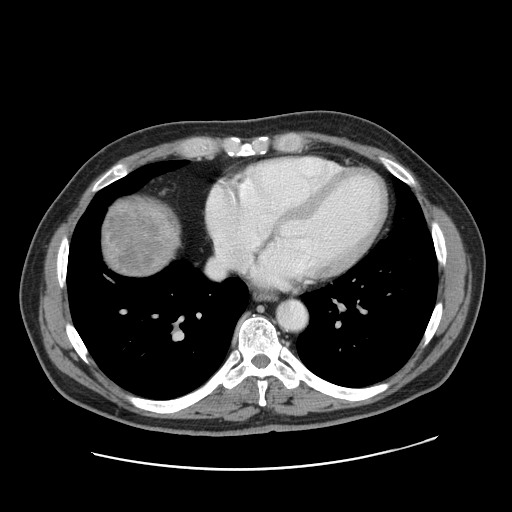
Contrast-enhanced abdominal CT, one axial slice. Position 161 of 178 along the scan axis. 120 kVp. Intravenous contrast given. Soft-tissue window (W 400 / L 40 HU). 512 × 512 image matrix, field of view 403 × 403 mm. Male patient, age 63 years. Case-level facts recorded for this patient, not image findings: diagnosis: colorectal cancer liver metastases, imaged before liver resection; multiple liver metastases: yes; largest metastasis: 8 cm; disease in both lobes: yes.
Structures marked on this image (outlined manually by an expert reader):
- liver: bounding box <101,200,178,277> (left, top, right, bottom; pixels)
- liver metastasis: <105,200,164,275>